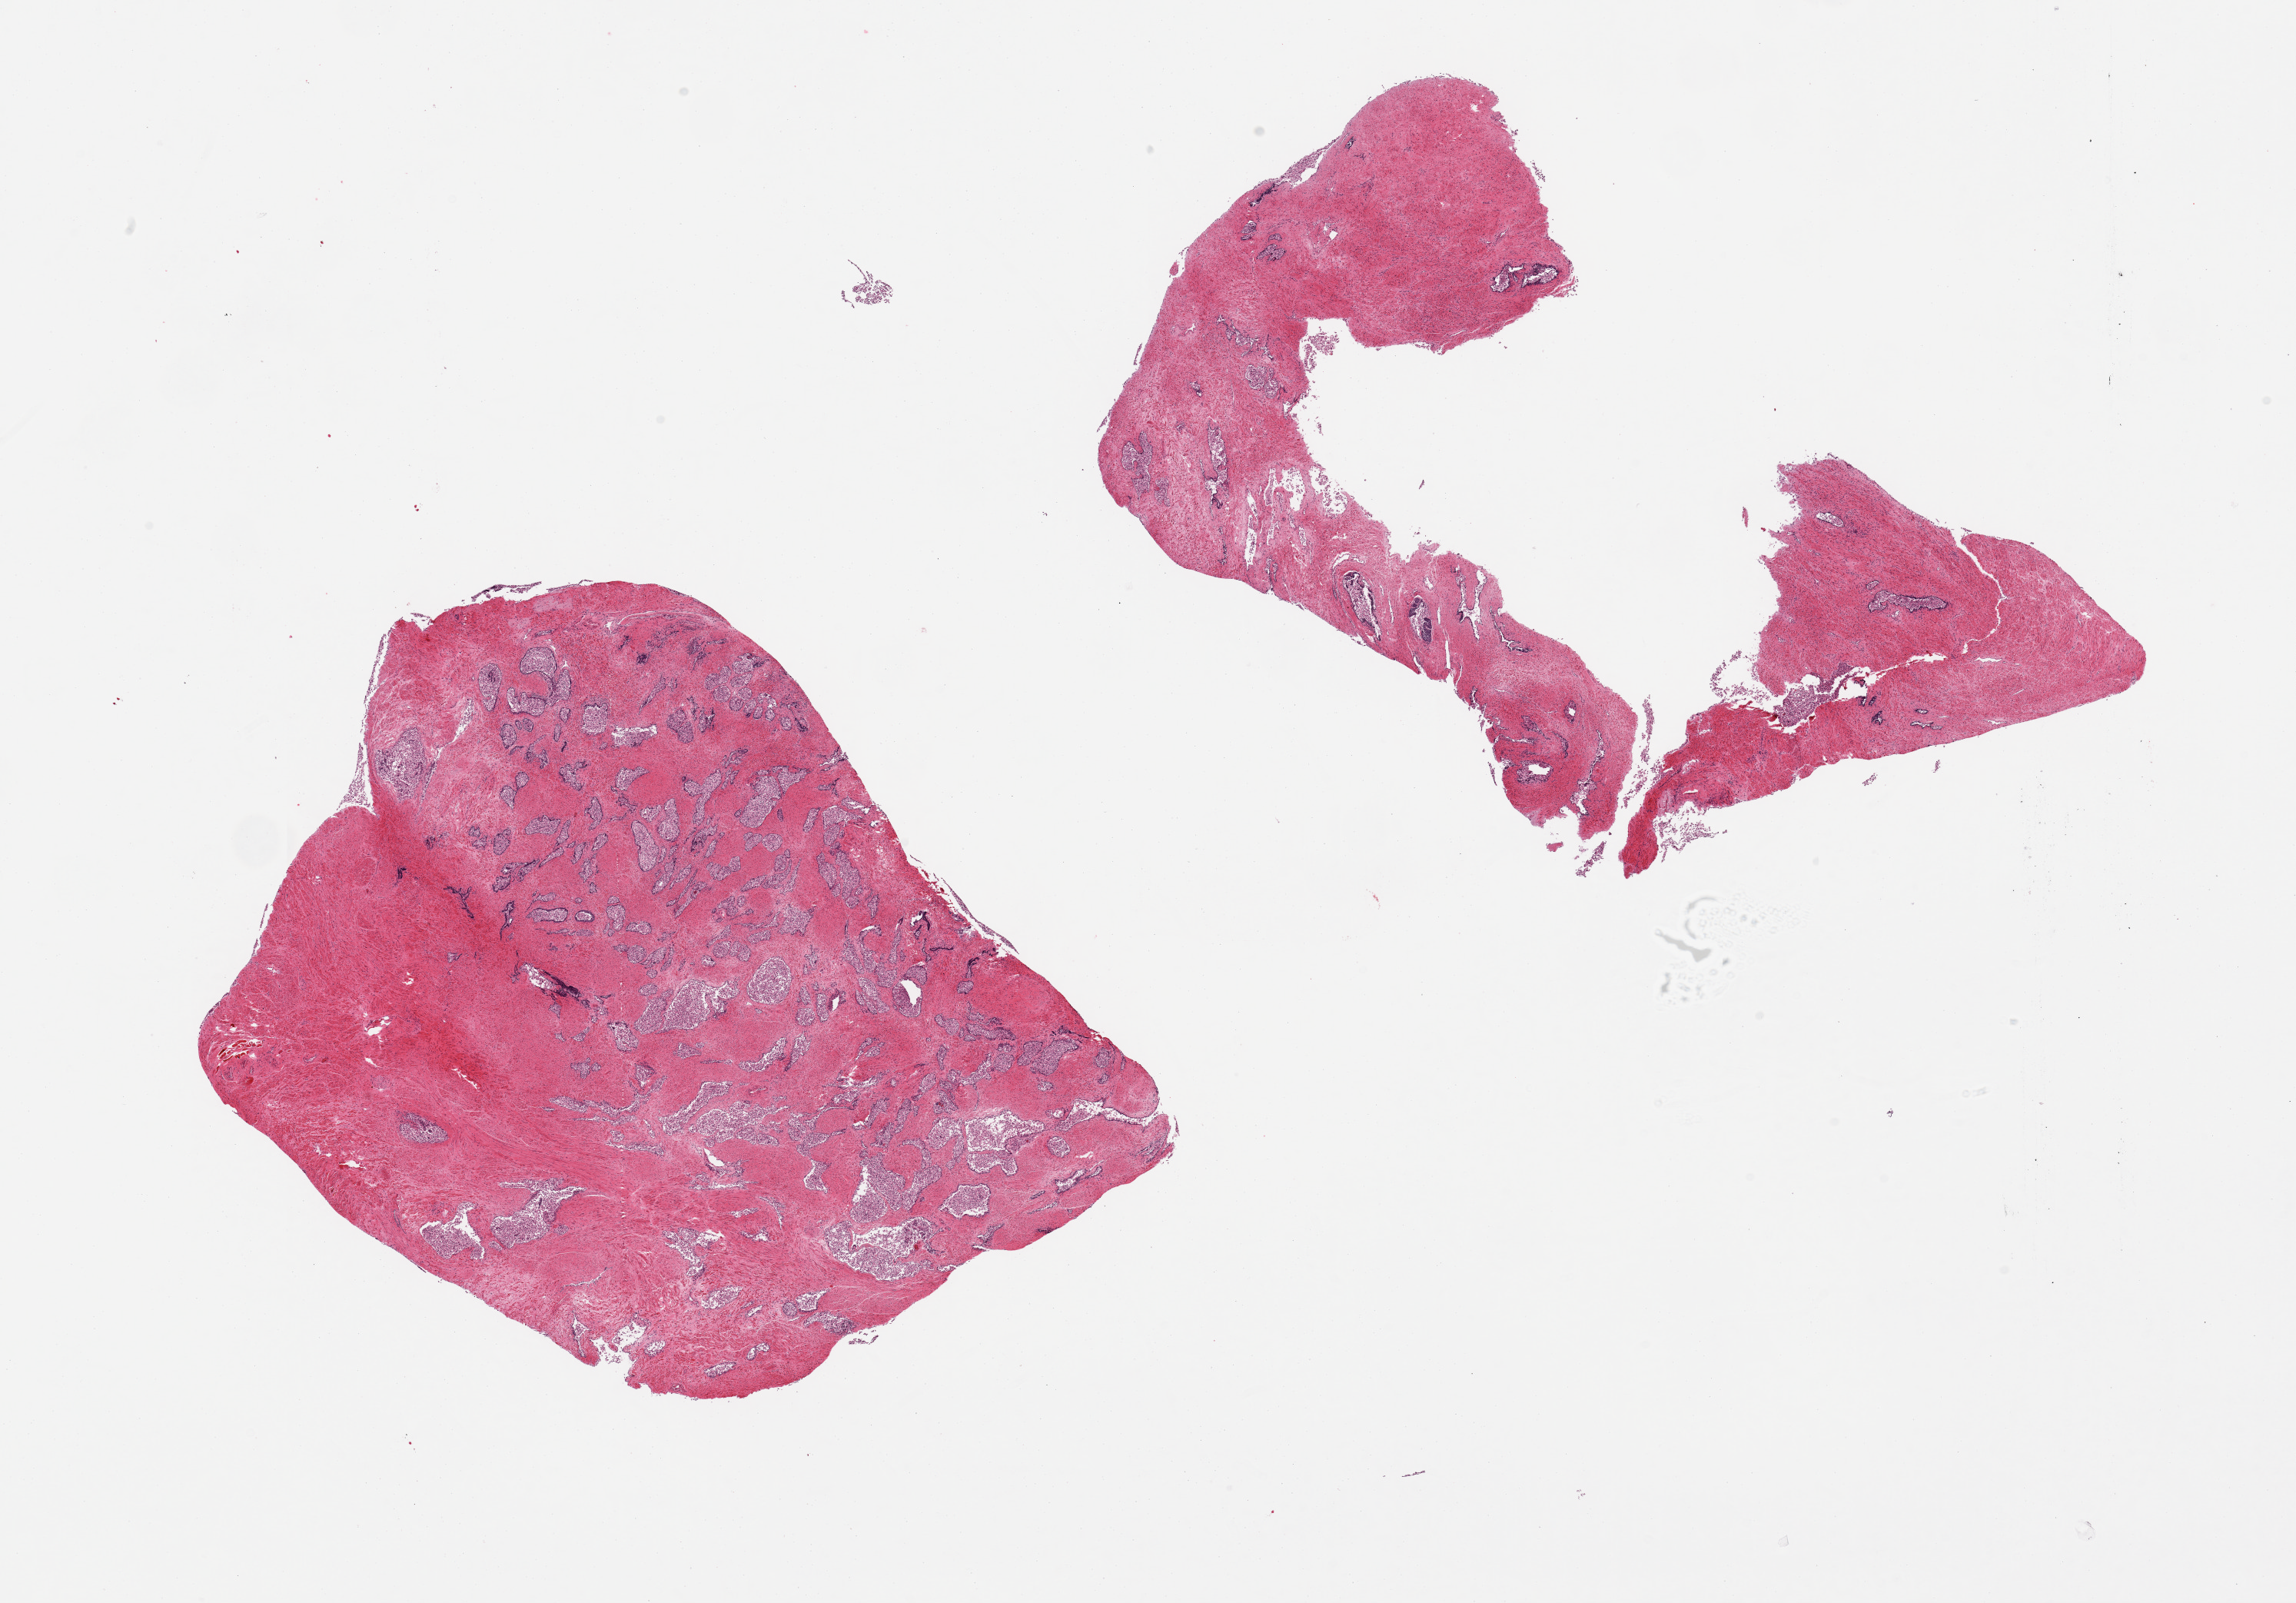
Haematoxylin and eosin whole-slide image — shown as a low-resolution overview of the whole scanned area (about 23.6 x 16.5 mm, from a 20x scan); PAXgene-fixed, paraffin-embedded tissue; target tissue: prostate; donor tissue sample. Donor: male.
Reviewer comment on this tissue sample: 2 pieces; glands autolyzed, stroma intact.